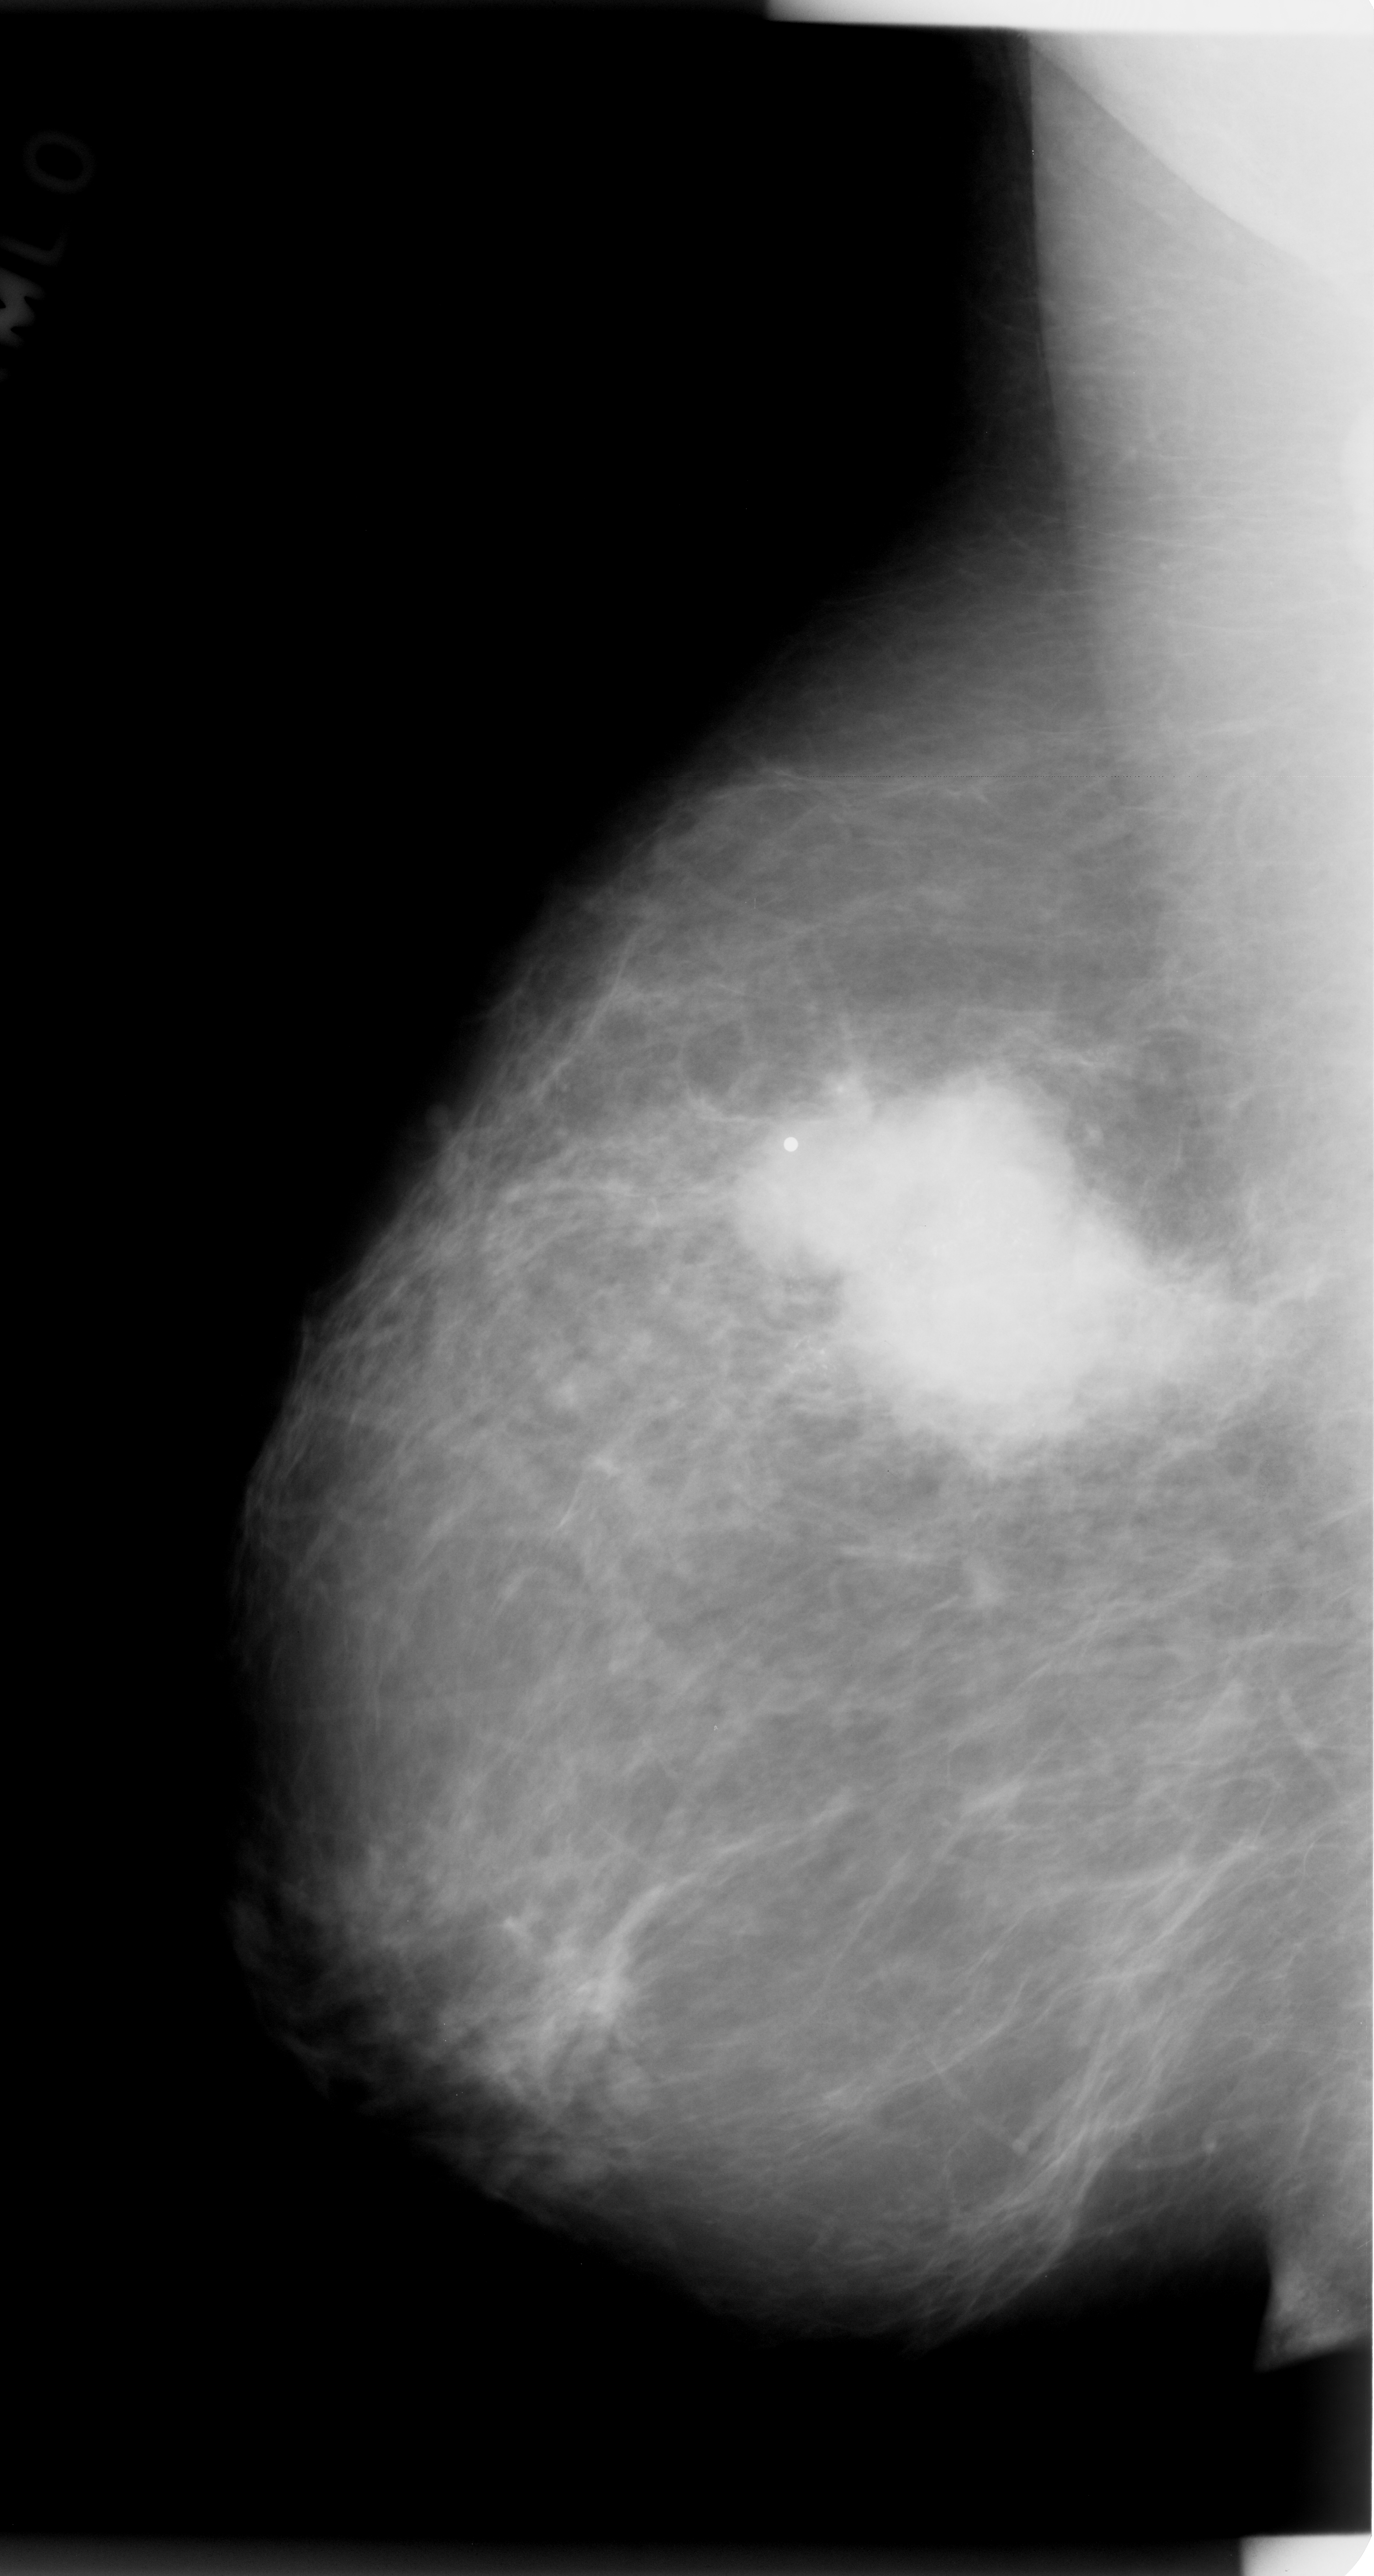
Digitized screen-film mammogram; right breast; mediolateral oblique (MLO) view; breast composition: almost entirely fatty (BI-RADS density category 1 of 4); 1374 × 2576 image matrix.
Expert-marked regions of interest on this image (one box per marked abnormality):
- calcifications, morphology pleomorphic, distribution clustered; BI-RADS assessment category 5; pathology result (as recorded, not read from the image): malignant: bounding box [x1, y1, x2, y2] px = [562, 887, 1364, 1773]